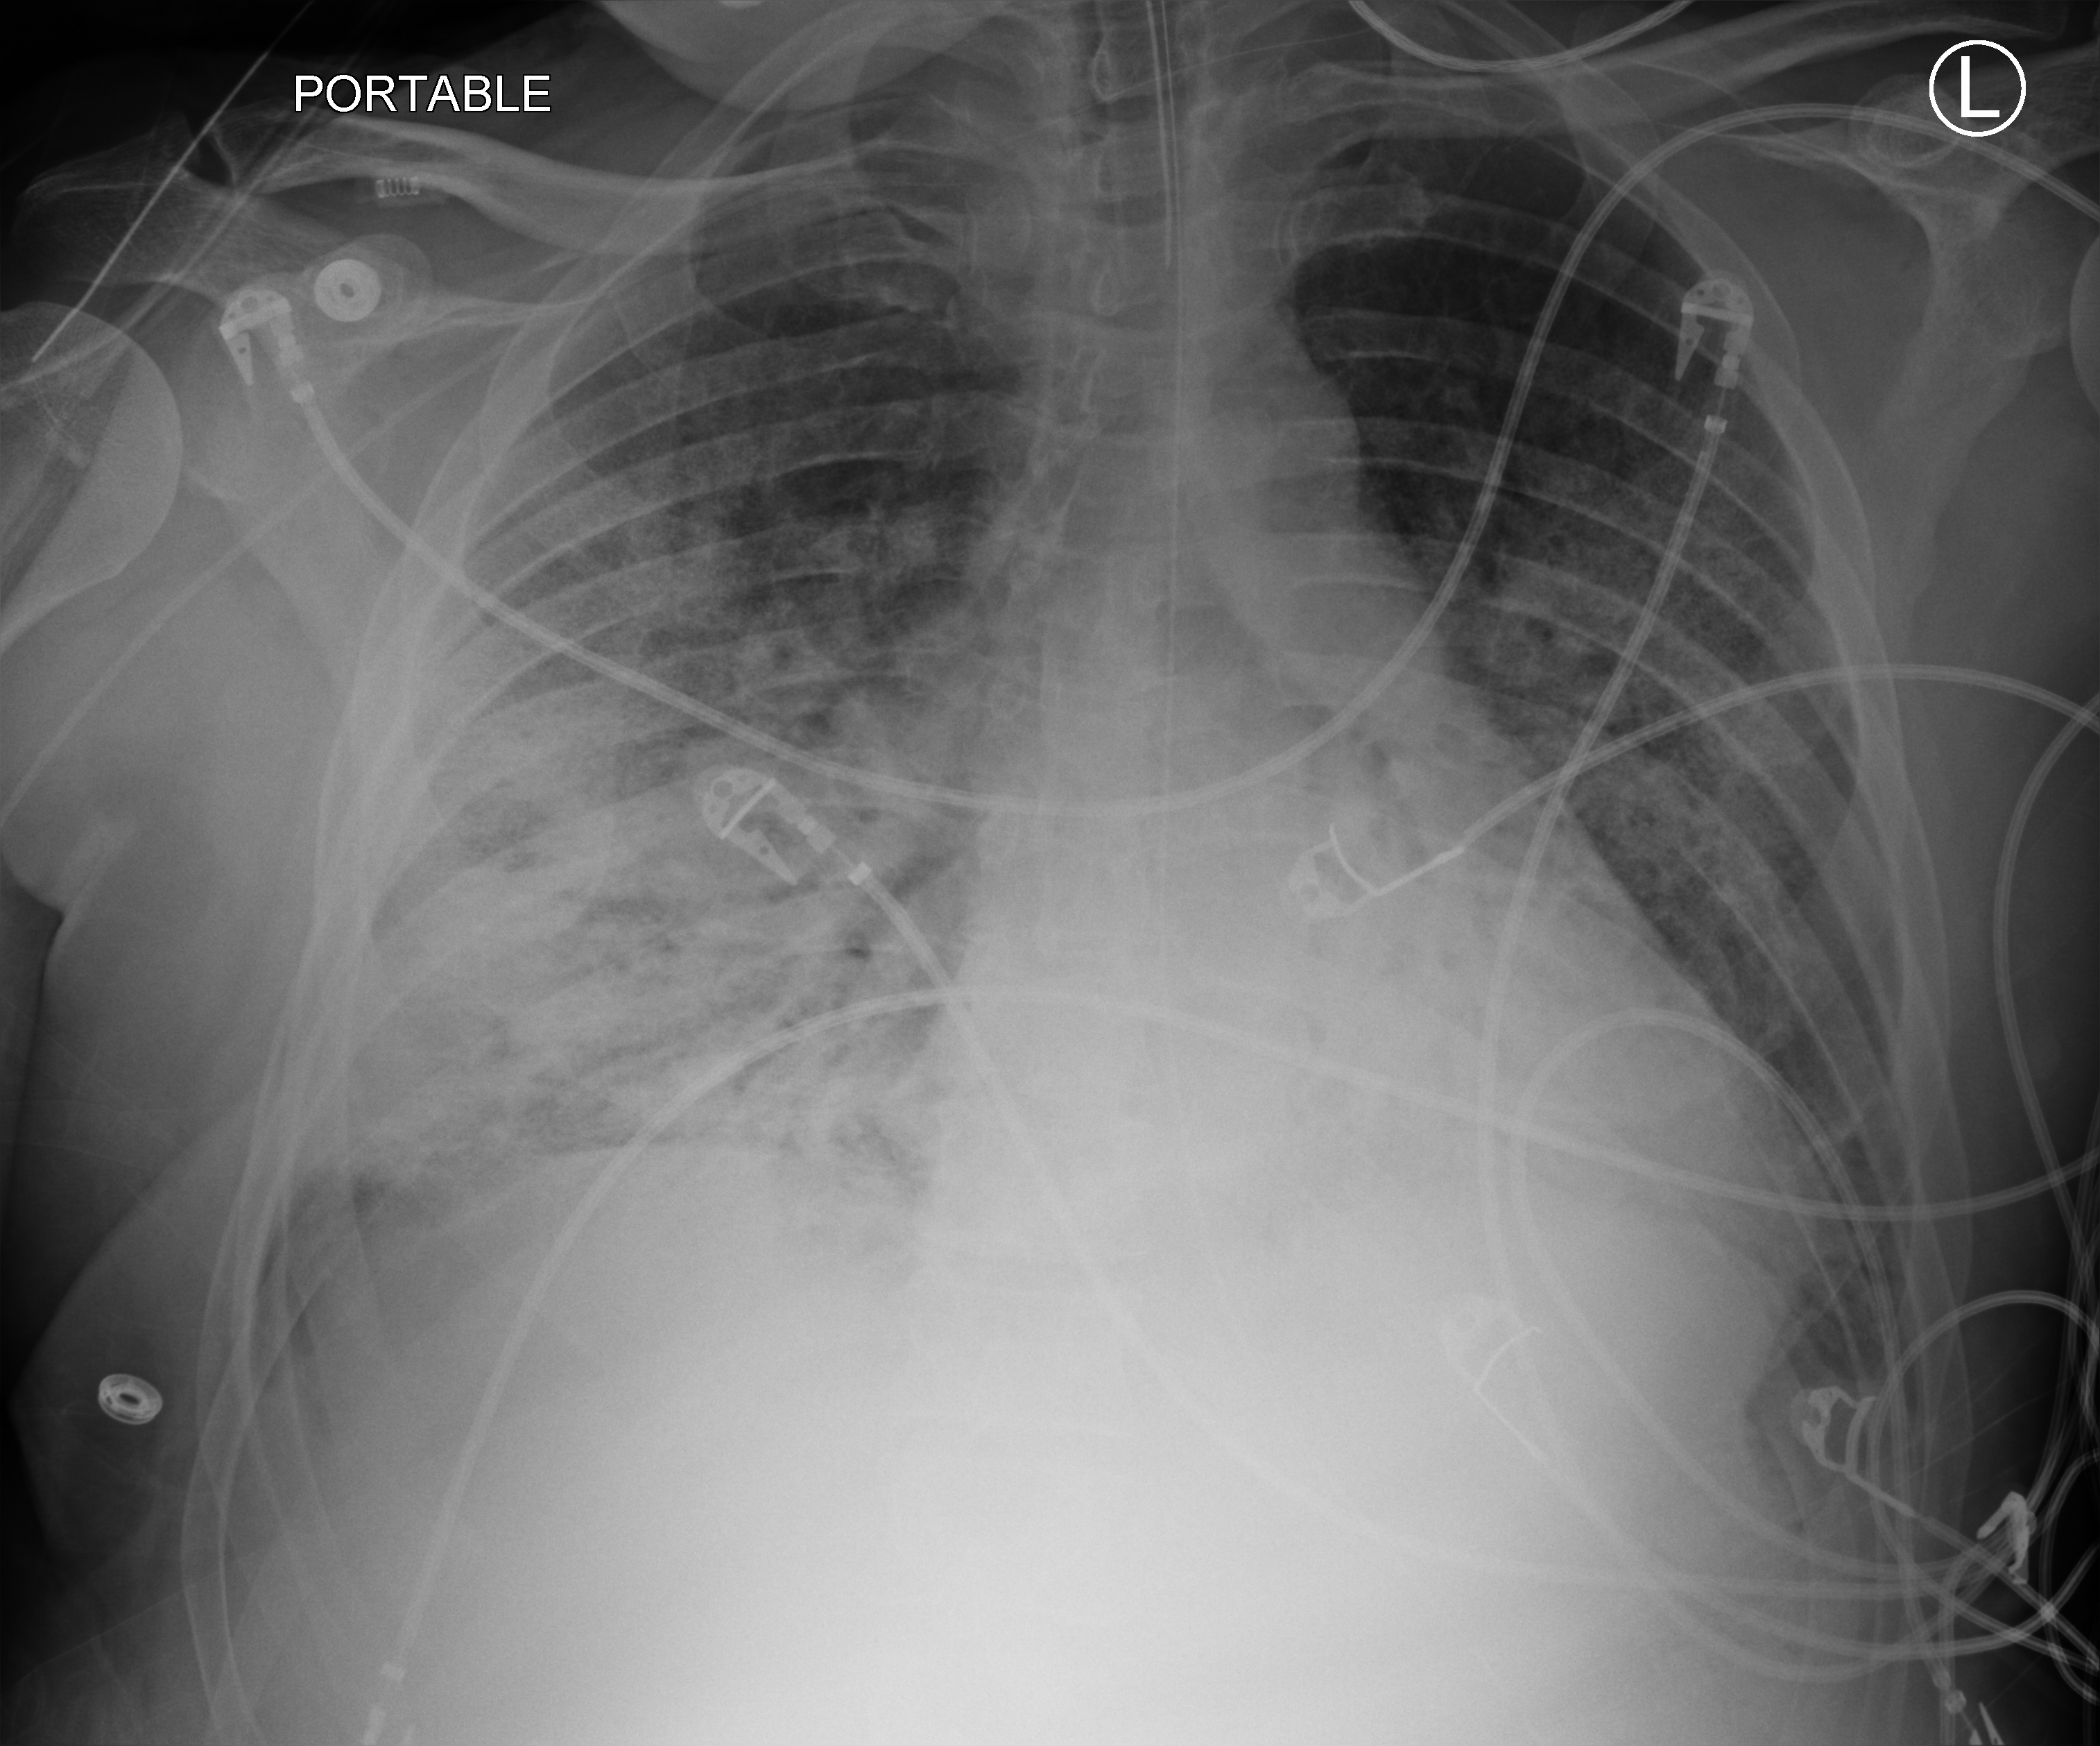
Bedside chest radiograph (computed radiography), anteroposterior (AP) projection. Male patient hospitalised with COVID-19, age 18–59 years.
From the hospital-stay record, not from the radiograph (when in the stay this image was taken is not recorded):
- admitted to intensive care during this hospital stay: yes